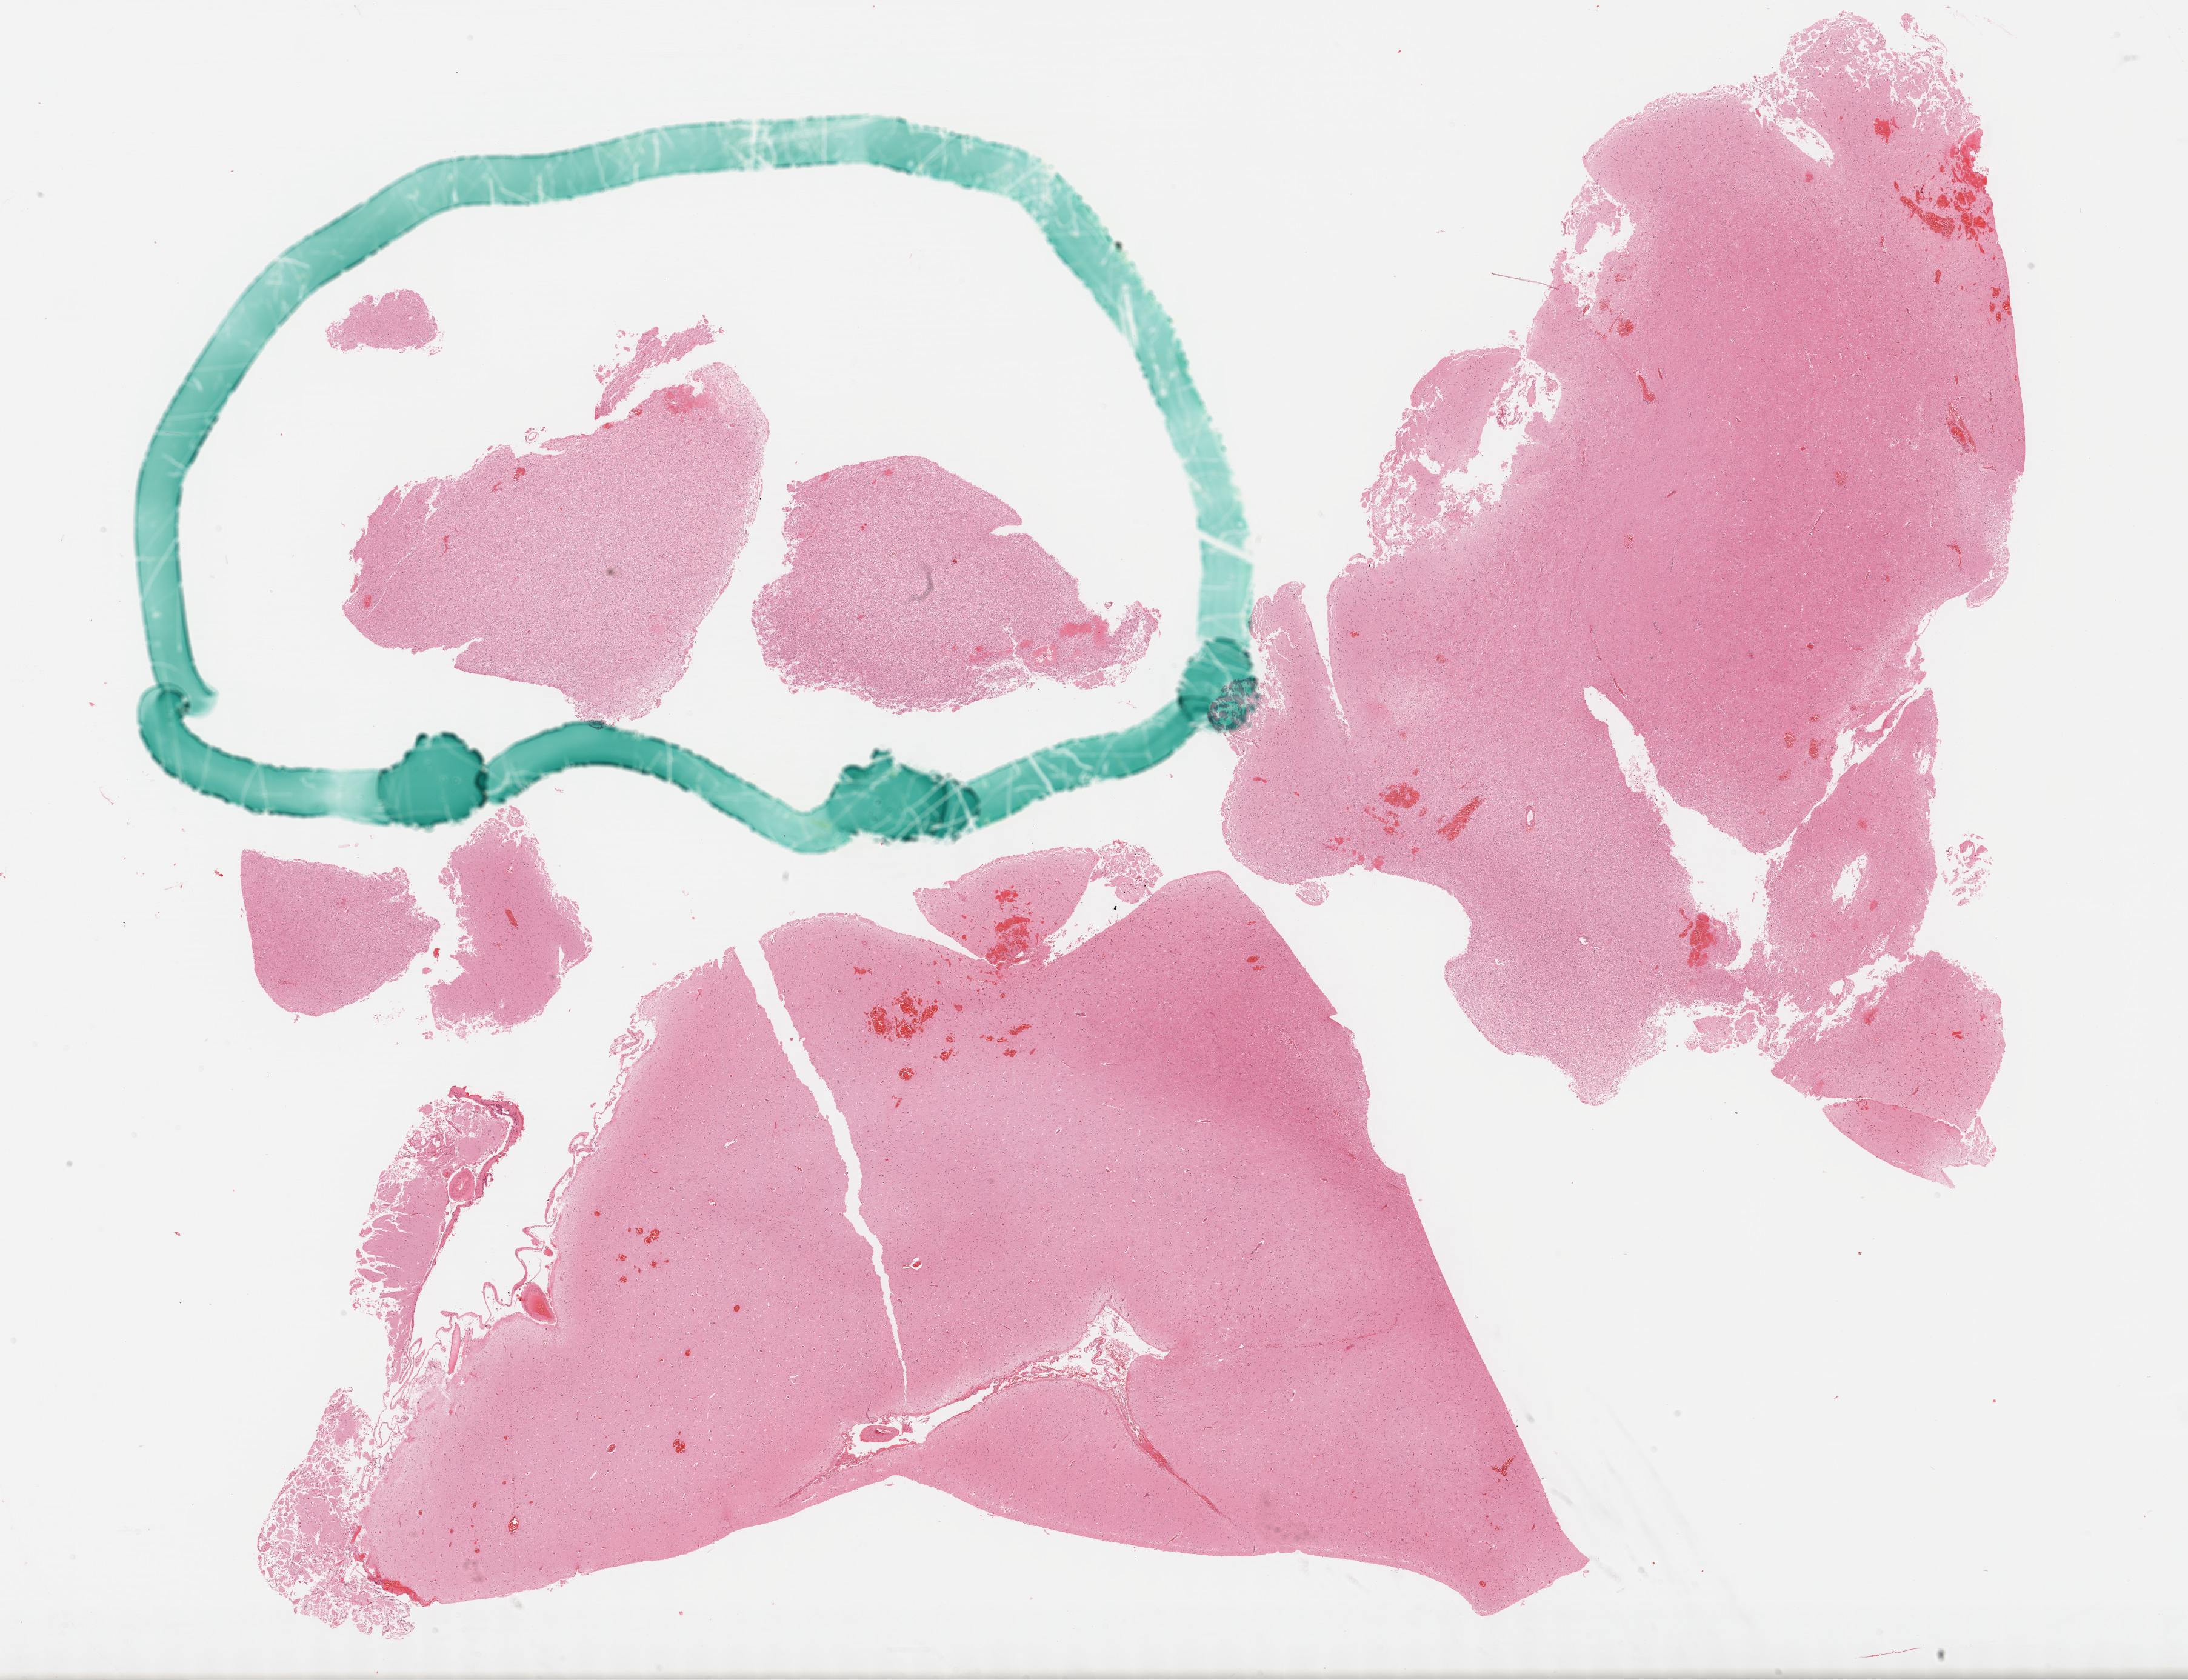
Digitized H&E tissue section (whole slide) — whole scanned area (about 29.2 x 22.4 mm, from a 40x scan) shown as a low-resolution overview; FFPE section; primary tumour sample from the brain. Patient: male, age at initial diagnosis 31 years.
Pathologic diagnosis: Mixed glioma (cerebrum).